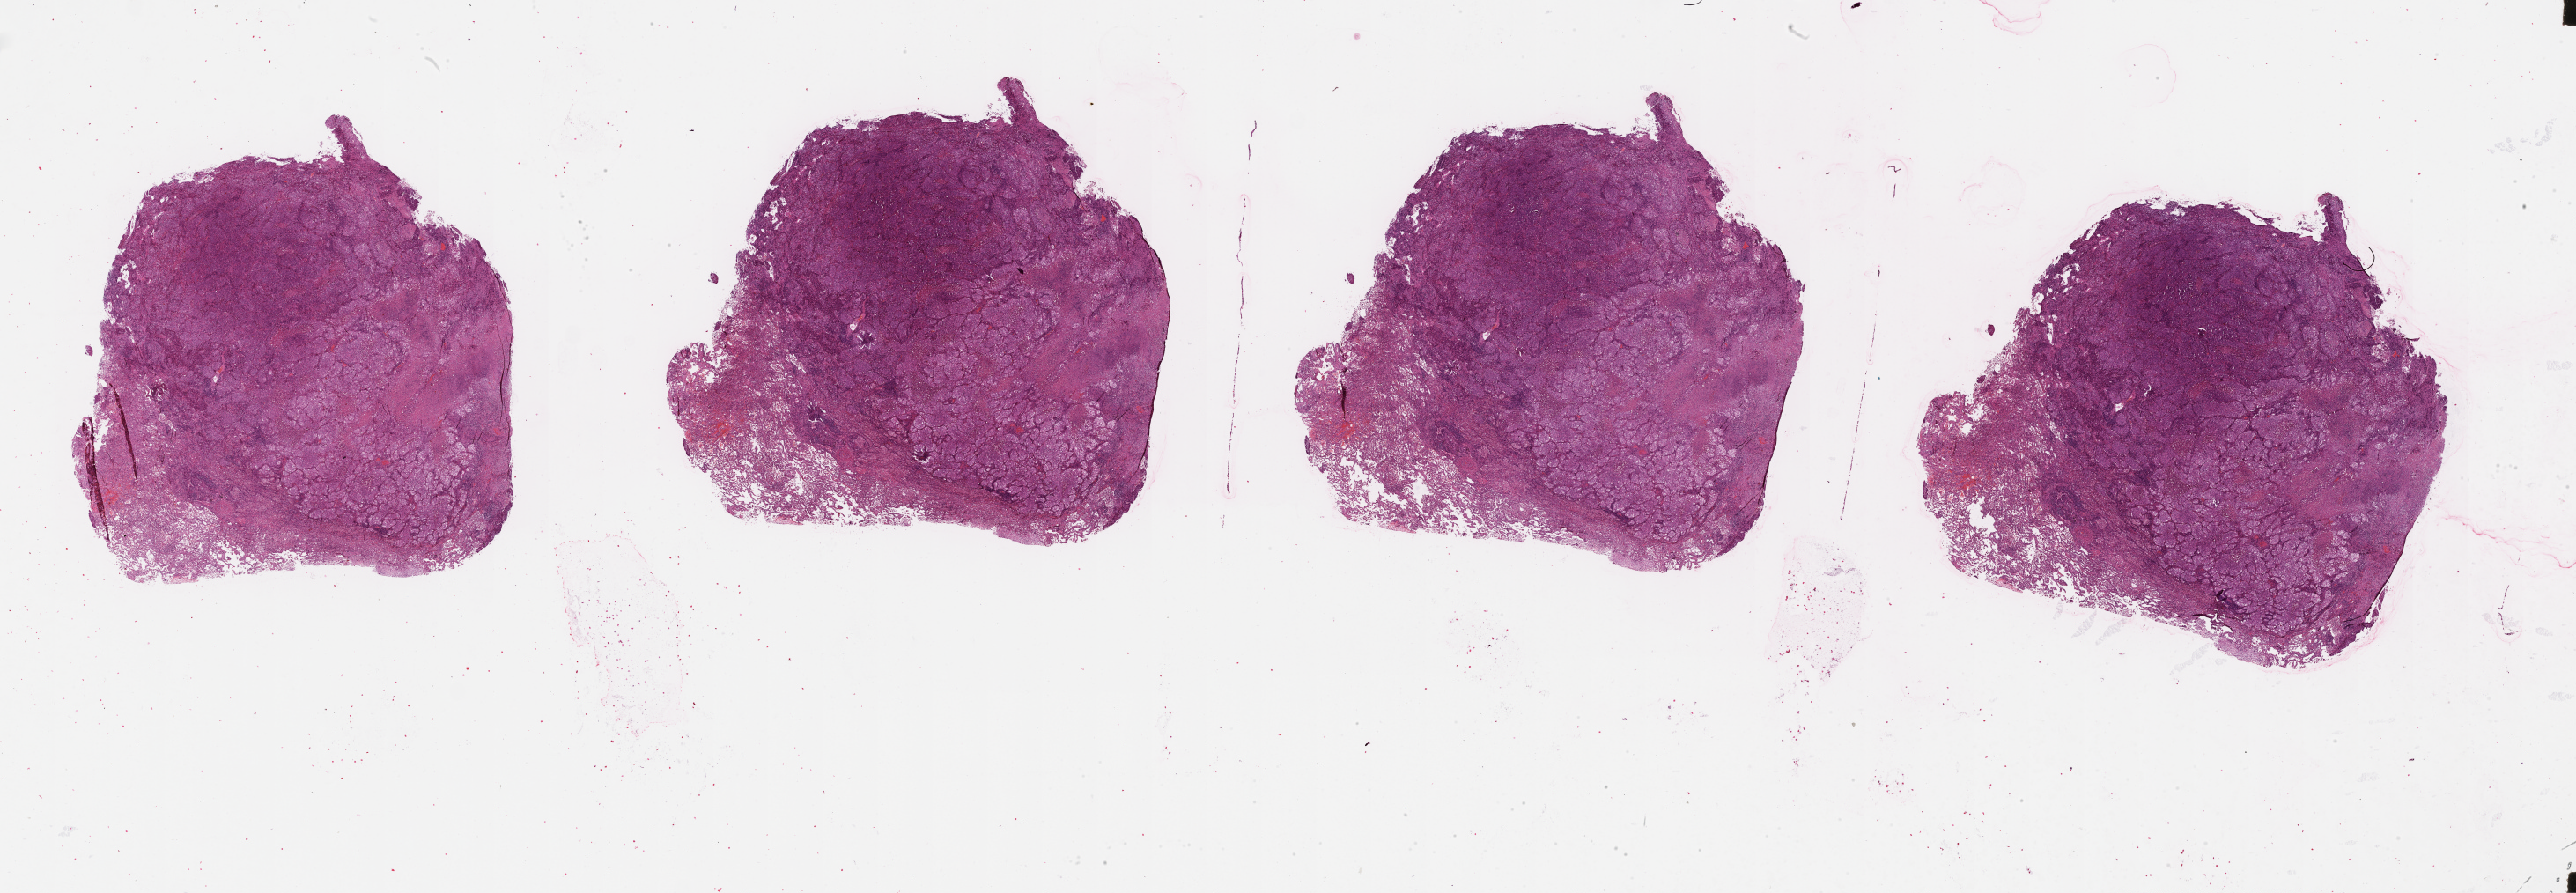
Whole-slide histology image, H&E-stained — shown as a low-resolution overview of the whole scanned area (about 47.1 x 16.3 mm, slide scanned at 20x). Lung, tissue type not recorded.
Patient diagnosis (cohort enrolment): lung adenocarcinoma (lung).